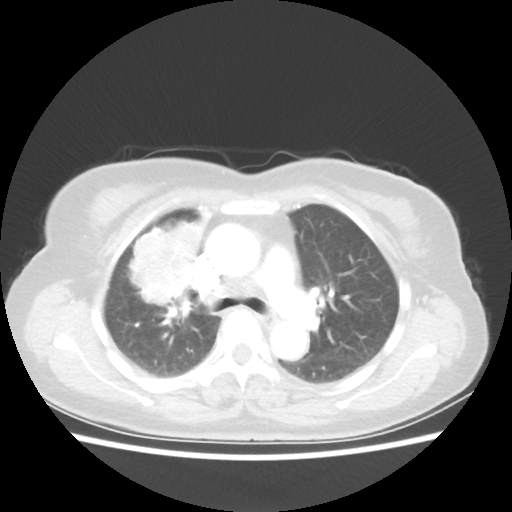
Chest CT, one axial slice; position 35 of 55 along the scan axis; reconstruction kernel STANDARD; 80 kVp; lung window (W 1500 / L -600 HU); 512 × 512 image matrix, field of view 337 × 337 mm. Patient: female, 62 years. Case-level facts recorded for this patient, not image findings: clinical TNM (as recorded): T4 N3 M0.
Annotated regions visible in this slice (bounding box drawn by a radiologist):
- lung tumour (recorded histology: squamous cell carcinoma): bounding box [x1, y1, x2, y2] px = [116, 211, 219, 314]